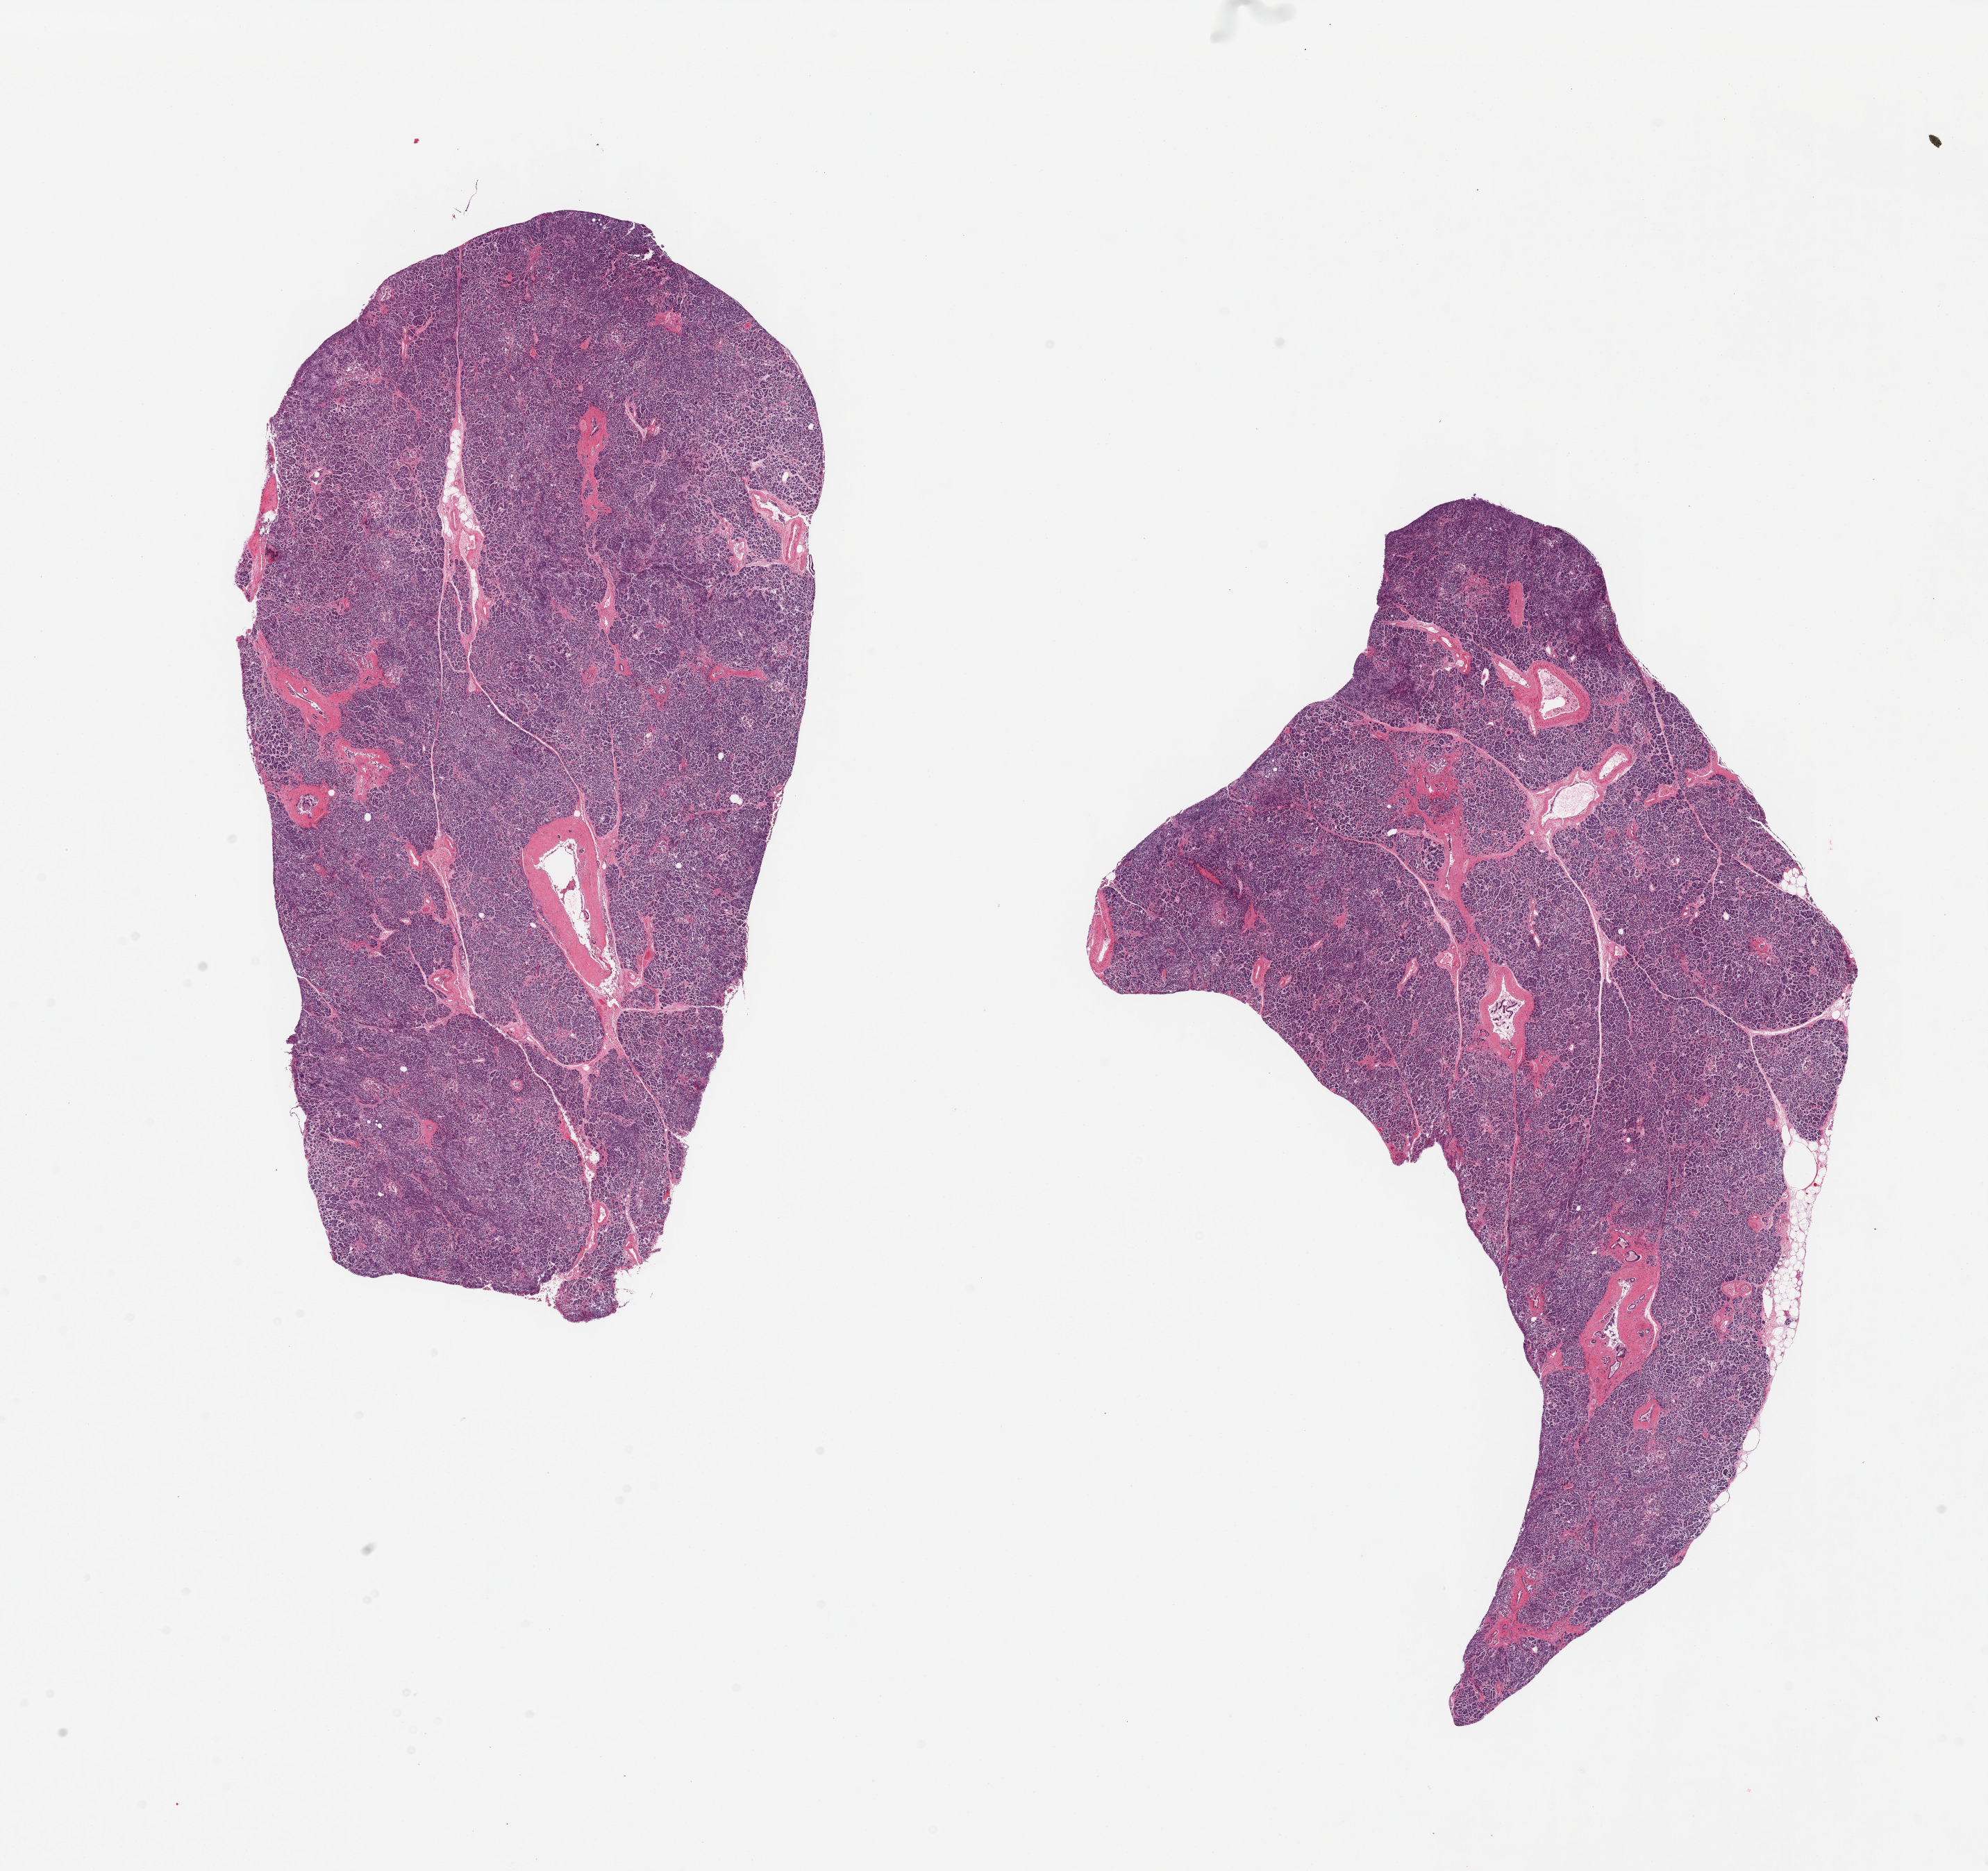
Haematoxylin and eosin whole-slide image, a low-resolution overview of the entire scanned area, about 22.6 x 21.3 mm; PAXgene-fixed paraffin-embedded (PFPE) section; target tissue: pancreas; donor tissue sample.
Pathologist's review note for this sample: 2 pieces, autolysis moderately-markedly advanced. Islets not well-preserved.